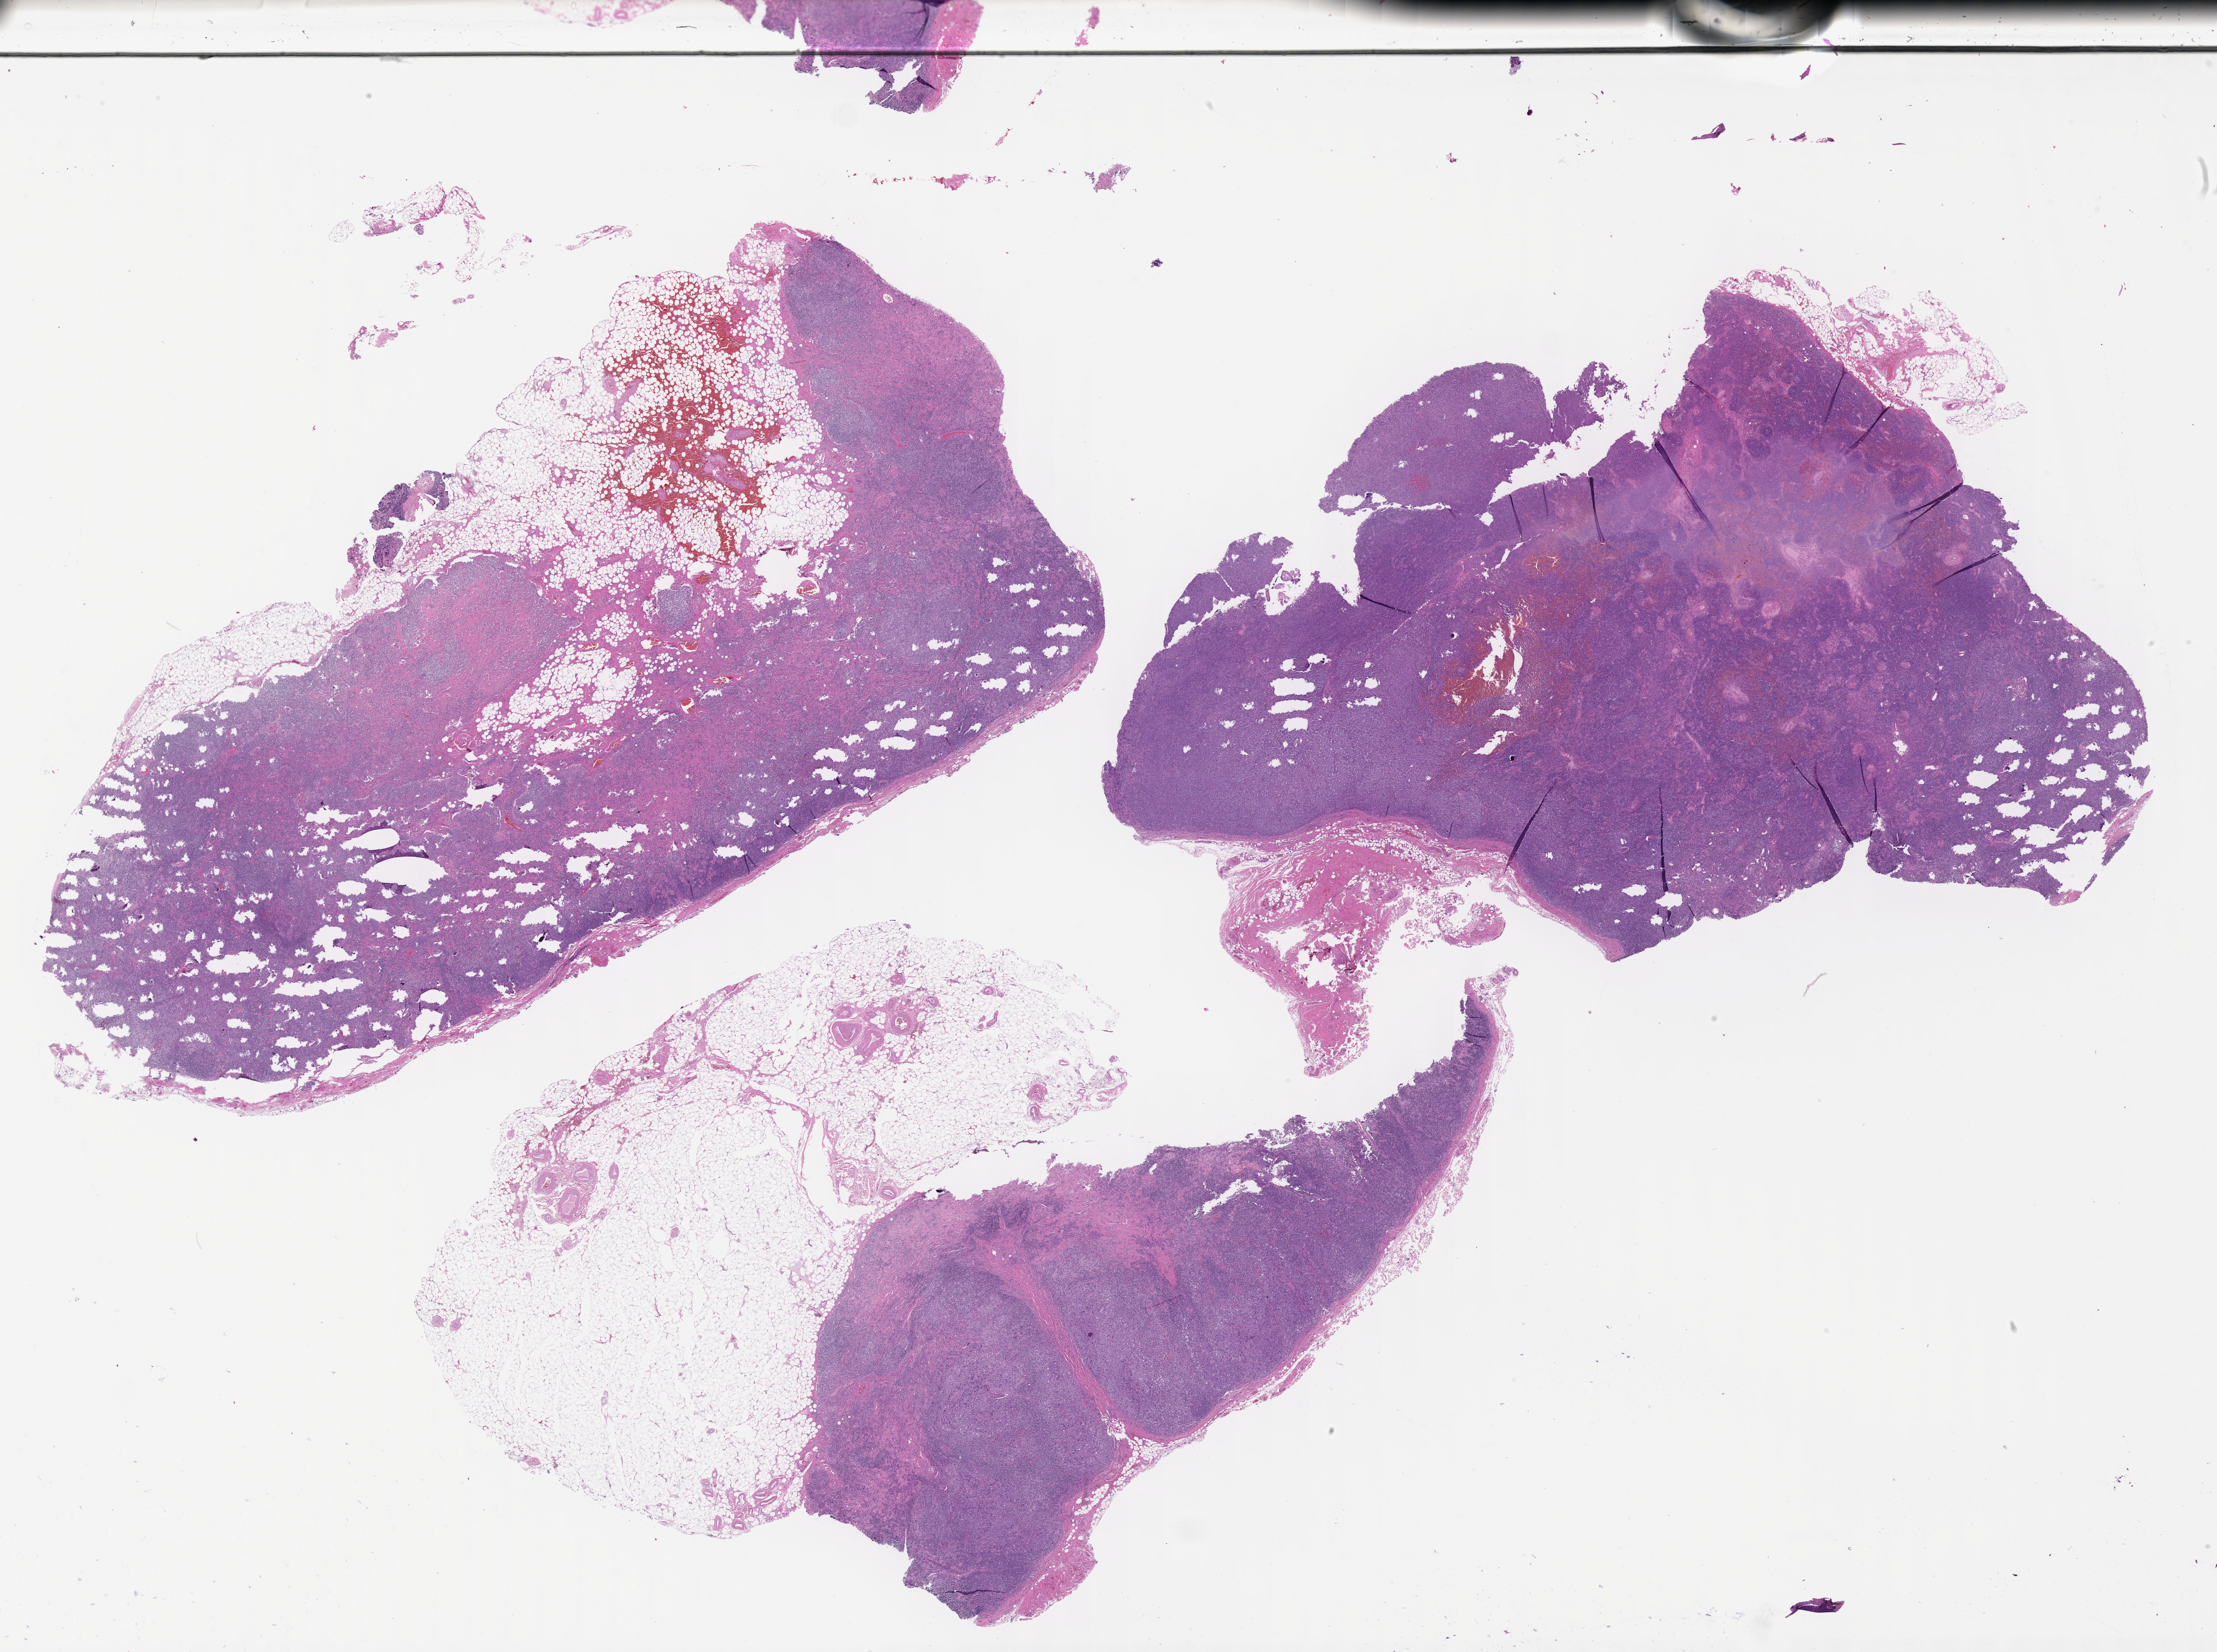
Digitized H&E-stained section — shown as a low-resolution overview of the whole scanned area (about 30.7 x 22.9 mm). Specimen: tumor tissue. Anatomic site: lymph node. Patient: male, 56 years old.
Diagnosis: Diffuse large B-cell lymphoma, NOS.